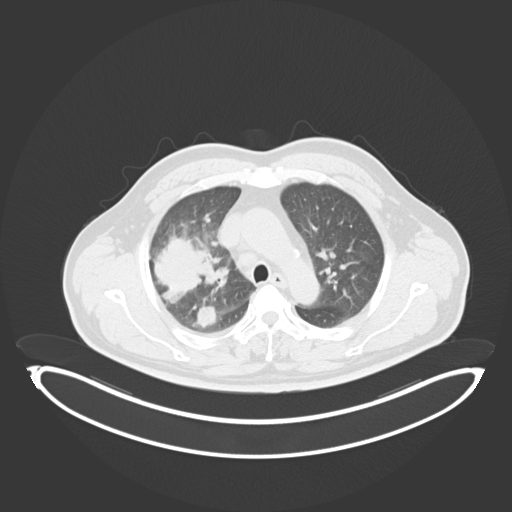
Chest CT, one axial slice; position 222 of 284 along the scan axis; reconstruction kernel B30f; lung window (W 1500 / L -600 HU); 3 mm slice thickness; 512 × 512 image matrix, field of view 500 × 500 mm. Patient: male, 55 years. From the clinical record (not read from this slice): clinical TNM (as recorded): T3 N2 M1.
Annotated regions visible in this slice (bounding box drawn by a radiologist):
- lung tumour (recorded histology: adenocarcinoma): bounding box (x1, y1, x2, y2) in pixels: (146, 227, 223, 301)